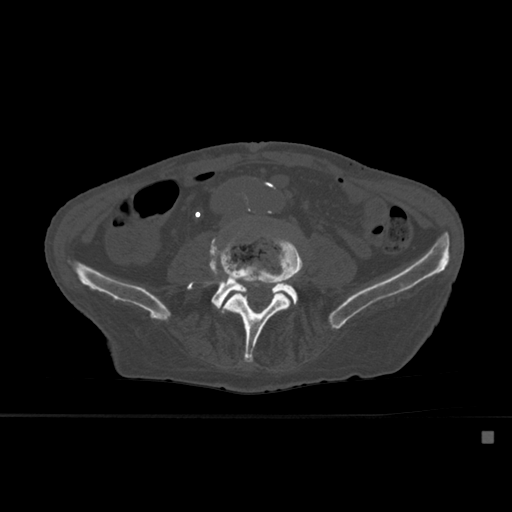
CT including the spine, one axial slice; slice 188 of 527 in the series (ordered by position); bone window (W 1800 / L 400 HU); 512 × 512 image matrix, field of view 373 × 373 mm. Patient: male, 78 years. Case-level facts recorded for this patient, not image findings: primary cancer: prostate.
Outlined on this slice (semi-automatic segmentation, software-assisted and operator-edited):
- L4 vertebra: bounding box (x1, y1, x2, y2) in pixels: (221, 234, 303, 362)
- L5 vertebra: (190, 232, 298, 309)